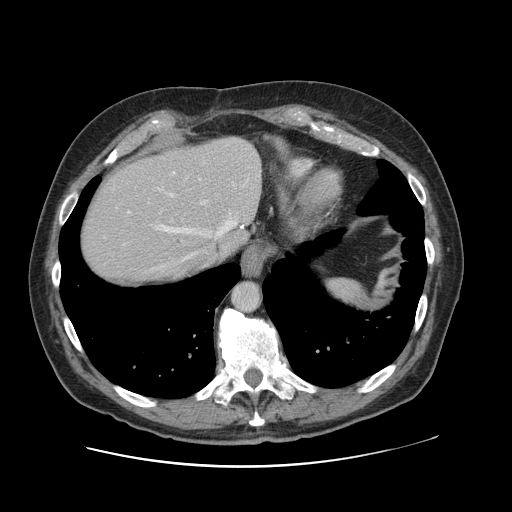
Contrast-enhanced abdominal CT, one axial slice. Position 99 of 138 along the scan axis. Intravenous contrast given. Soft-tissue window (W 400 / L 40 HU). 512 × 512 image matrix. Male patient, age 71 years. Case-level facts recorded for this patient, not image findings: diagnosis: colorectal cancer liver metastases, imaged before liver resection; multiple liver metastases: no; largest metastasis: 3.3 cm; disease in both lobes: no.
Outlined on this slice (outlined manually by an expert reader):
- hepatic veins: box from (x=160, y=212) to (x=243, y=267) px
- liver: (x=80, y=138)–(x=261, y=287)
- planned liver remnant (the part of the liver to remain after resection): (x=80, y=161)–(x=223, y=287)